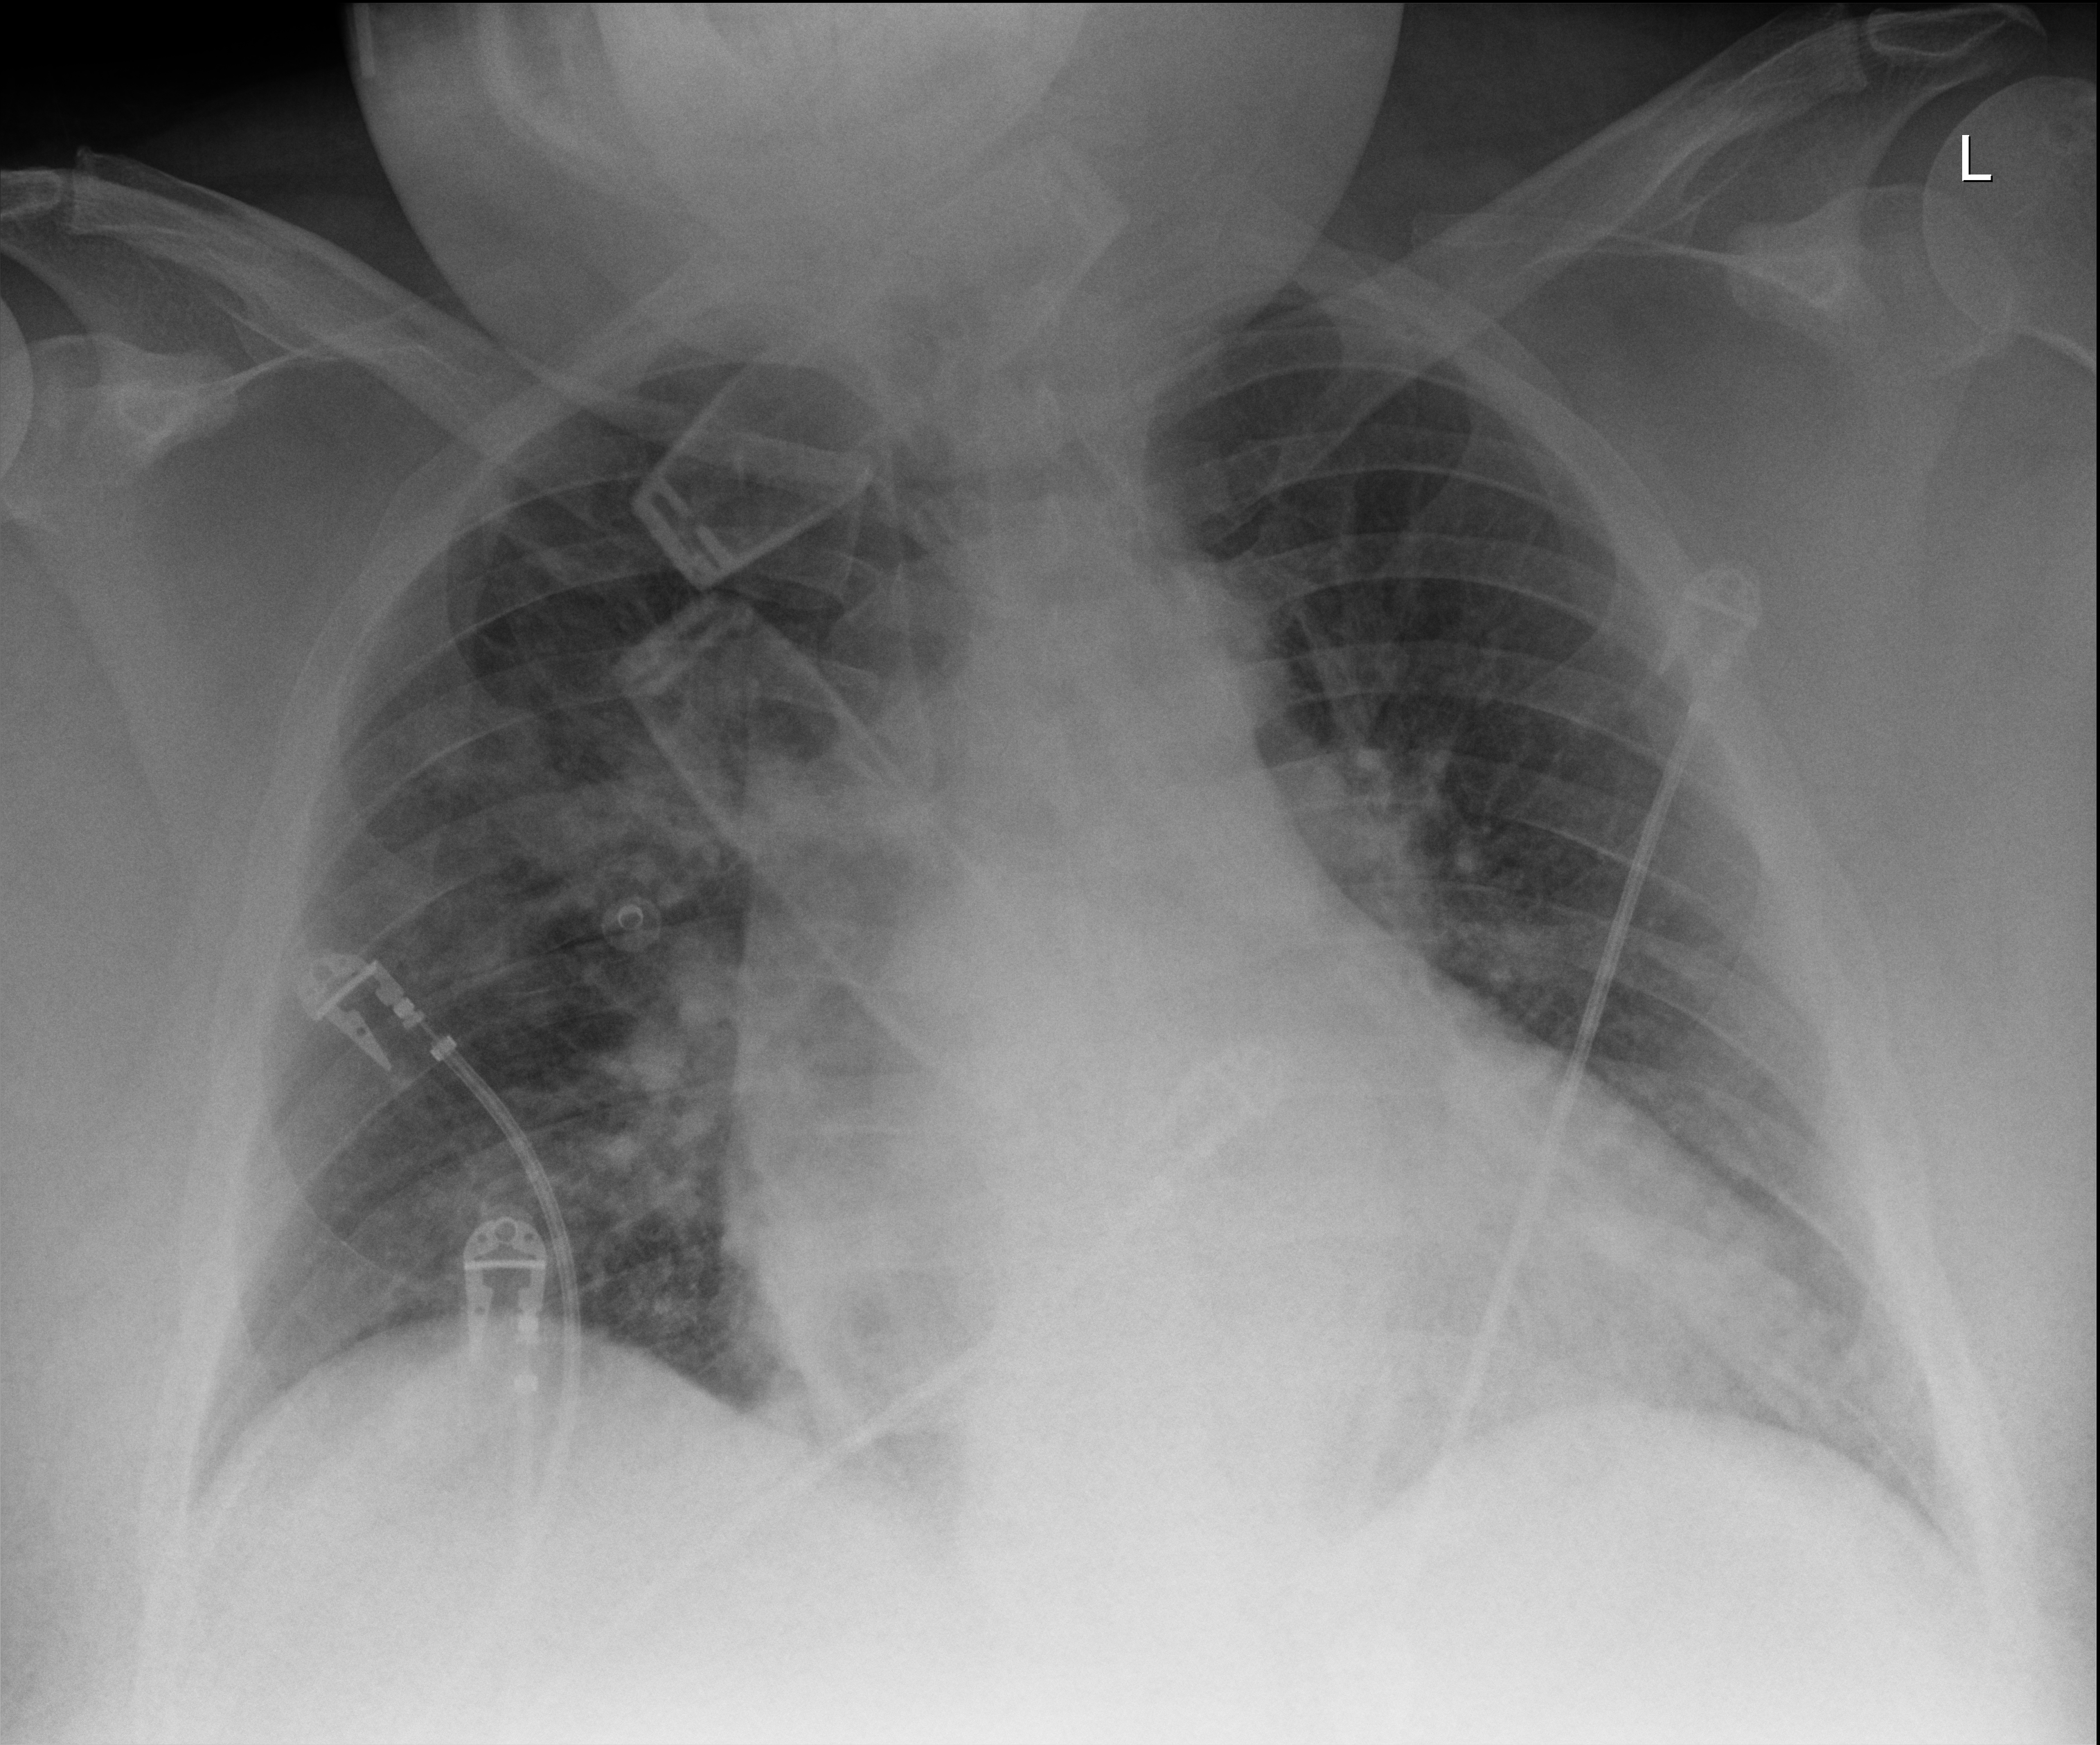
Chest X-ray (portable); anteroposterior (AP) projection. Male patient hospitalised with COVID-19, age 18–59 years.
Admission-level facts for this patient (not findings on this image; timing relative to this image not recorded):
- chronic kidney disease (admission record): no
- mechanically ventilated during this hospital stay: no
- admitted to intensive care during this hospital stay: no